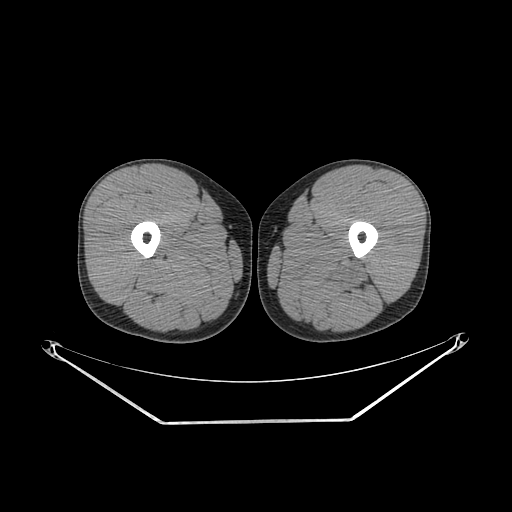
CT of an extremity soft-tissue mass (from a PET/CT study), one axial slice; slice 236 of 267 in the series (ordered by position); reconstruction kernel SOFT; 140 kVp; soft-tissue window (W 400 / L 40 HU); 3.75 mm slice thickness; 512 × 512 image matrix. Male patient. From the clinical record (not read from this slice): histological type: extraskeletal osteosarcoma; grade: high; site of the primary tumour: left adductur.
Structures marked on this image (expert contour drawn on MRI and transferred to this co-registered scan by the dataset authors):
- gross tumour volume (mass): bounding box [x1, y1, x2, y2] px = [272, 246, 380, 295]